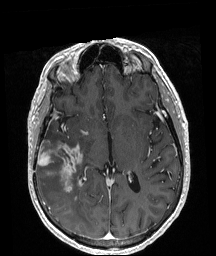
Brain MRI from a brain-tumour surgery series, one axial slice; position 105 of 208 along the scan axis; T1-weighted post-contrast; 1 mm slice thickness; 216 × 256 image matrix, field of view 211 × 250 mm. From the clinical record (not read from this slice): histopathology: Astrocytoma; WHO grade: 4; IDH mutation: yes; tumour location: Right Temporal.
Annotated regions visible in this slice (manually delineated by an expert):
- tumour: bounding box [x1, y1, x2, y2] px = [38, 143, 82, 192]